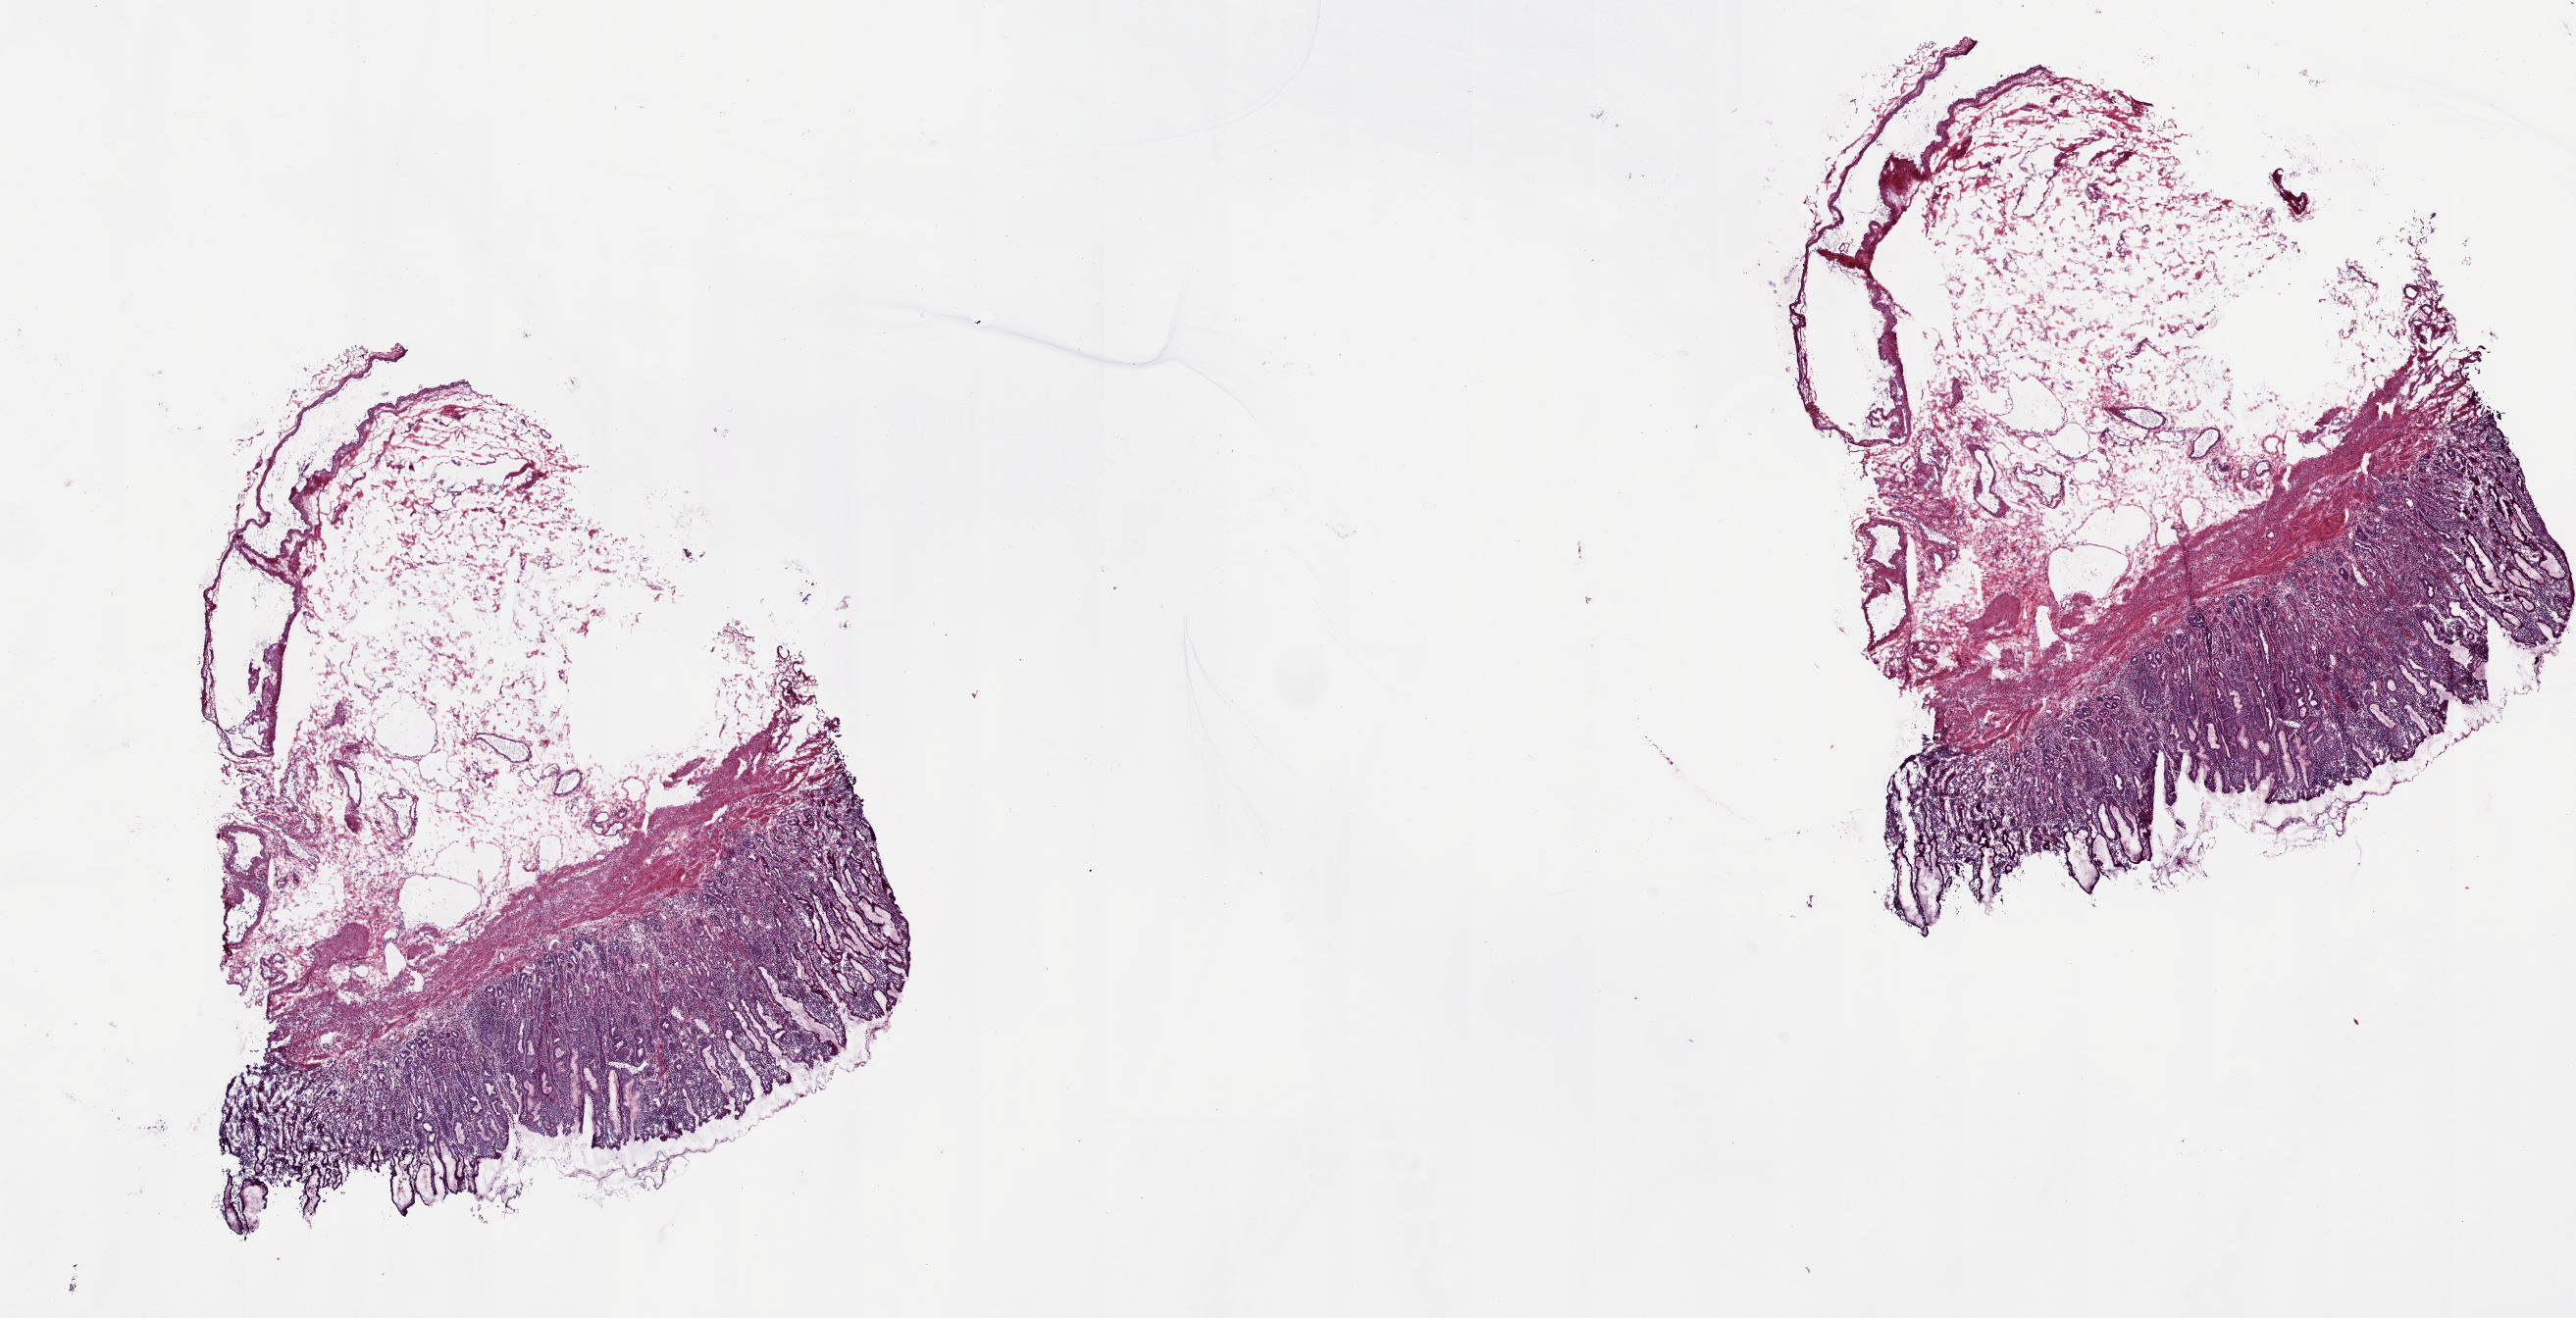
Hematoxylin and eosin (H&E) stained whole-slide image — a low-resolution overview of the entire scanned area, about 20.8 x 10.7 mm; frozen section from the top of the tissue portion; sample: solid tissue normal (non-tumour tissue), esophagus. Patient: male, age at initial diagnosis 77 years. Slide review estimates, as recorded: tumour cells 0%, tumour nuclei 0%, normal cells 100%, stromal cells 0%, necrosis 0%. Inflammatory infiltration, as recorded: lymphocyte infiltration 0%, monocyte infiltration 0%, neutrophil infiltration 0%.
This section: solid tissue normal sample (biorepository sample class). Patient diagnosis: Adenocarcinoma, NOS (lower third of esophagus).